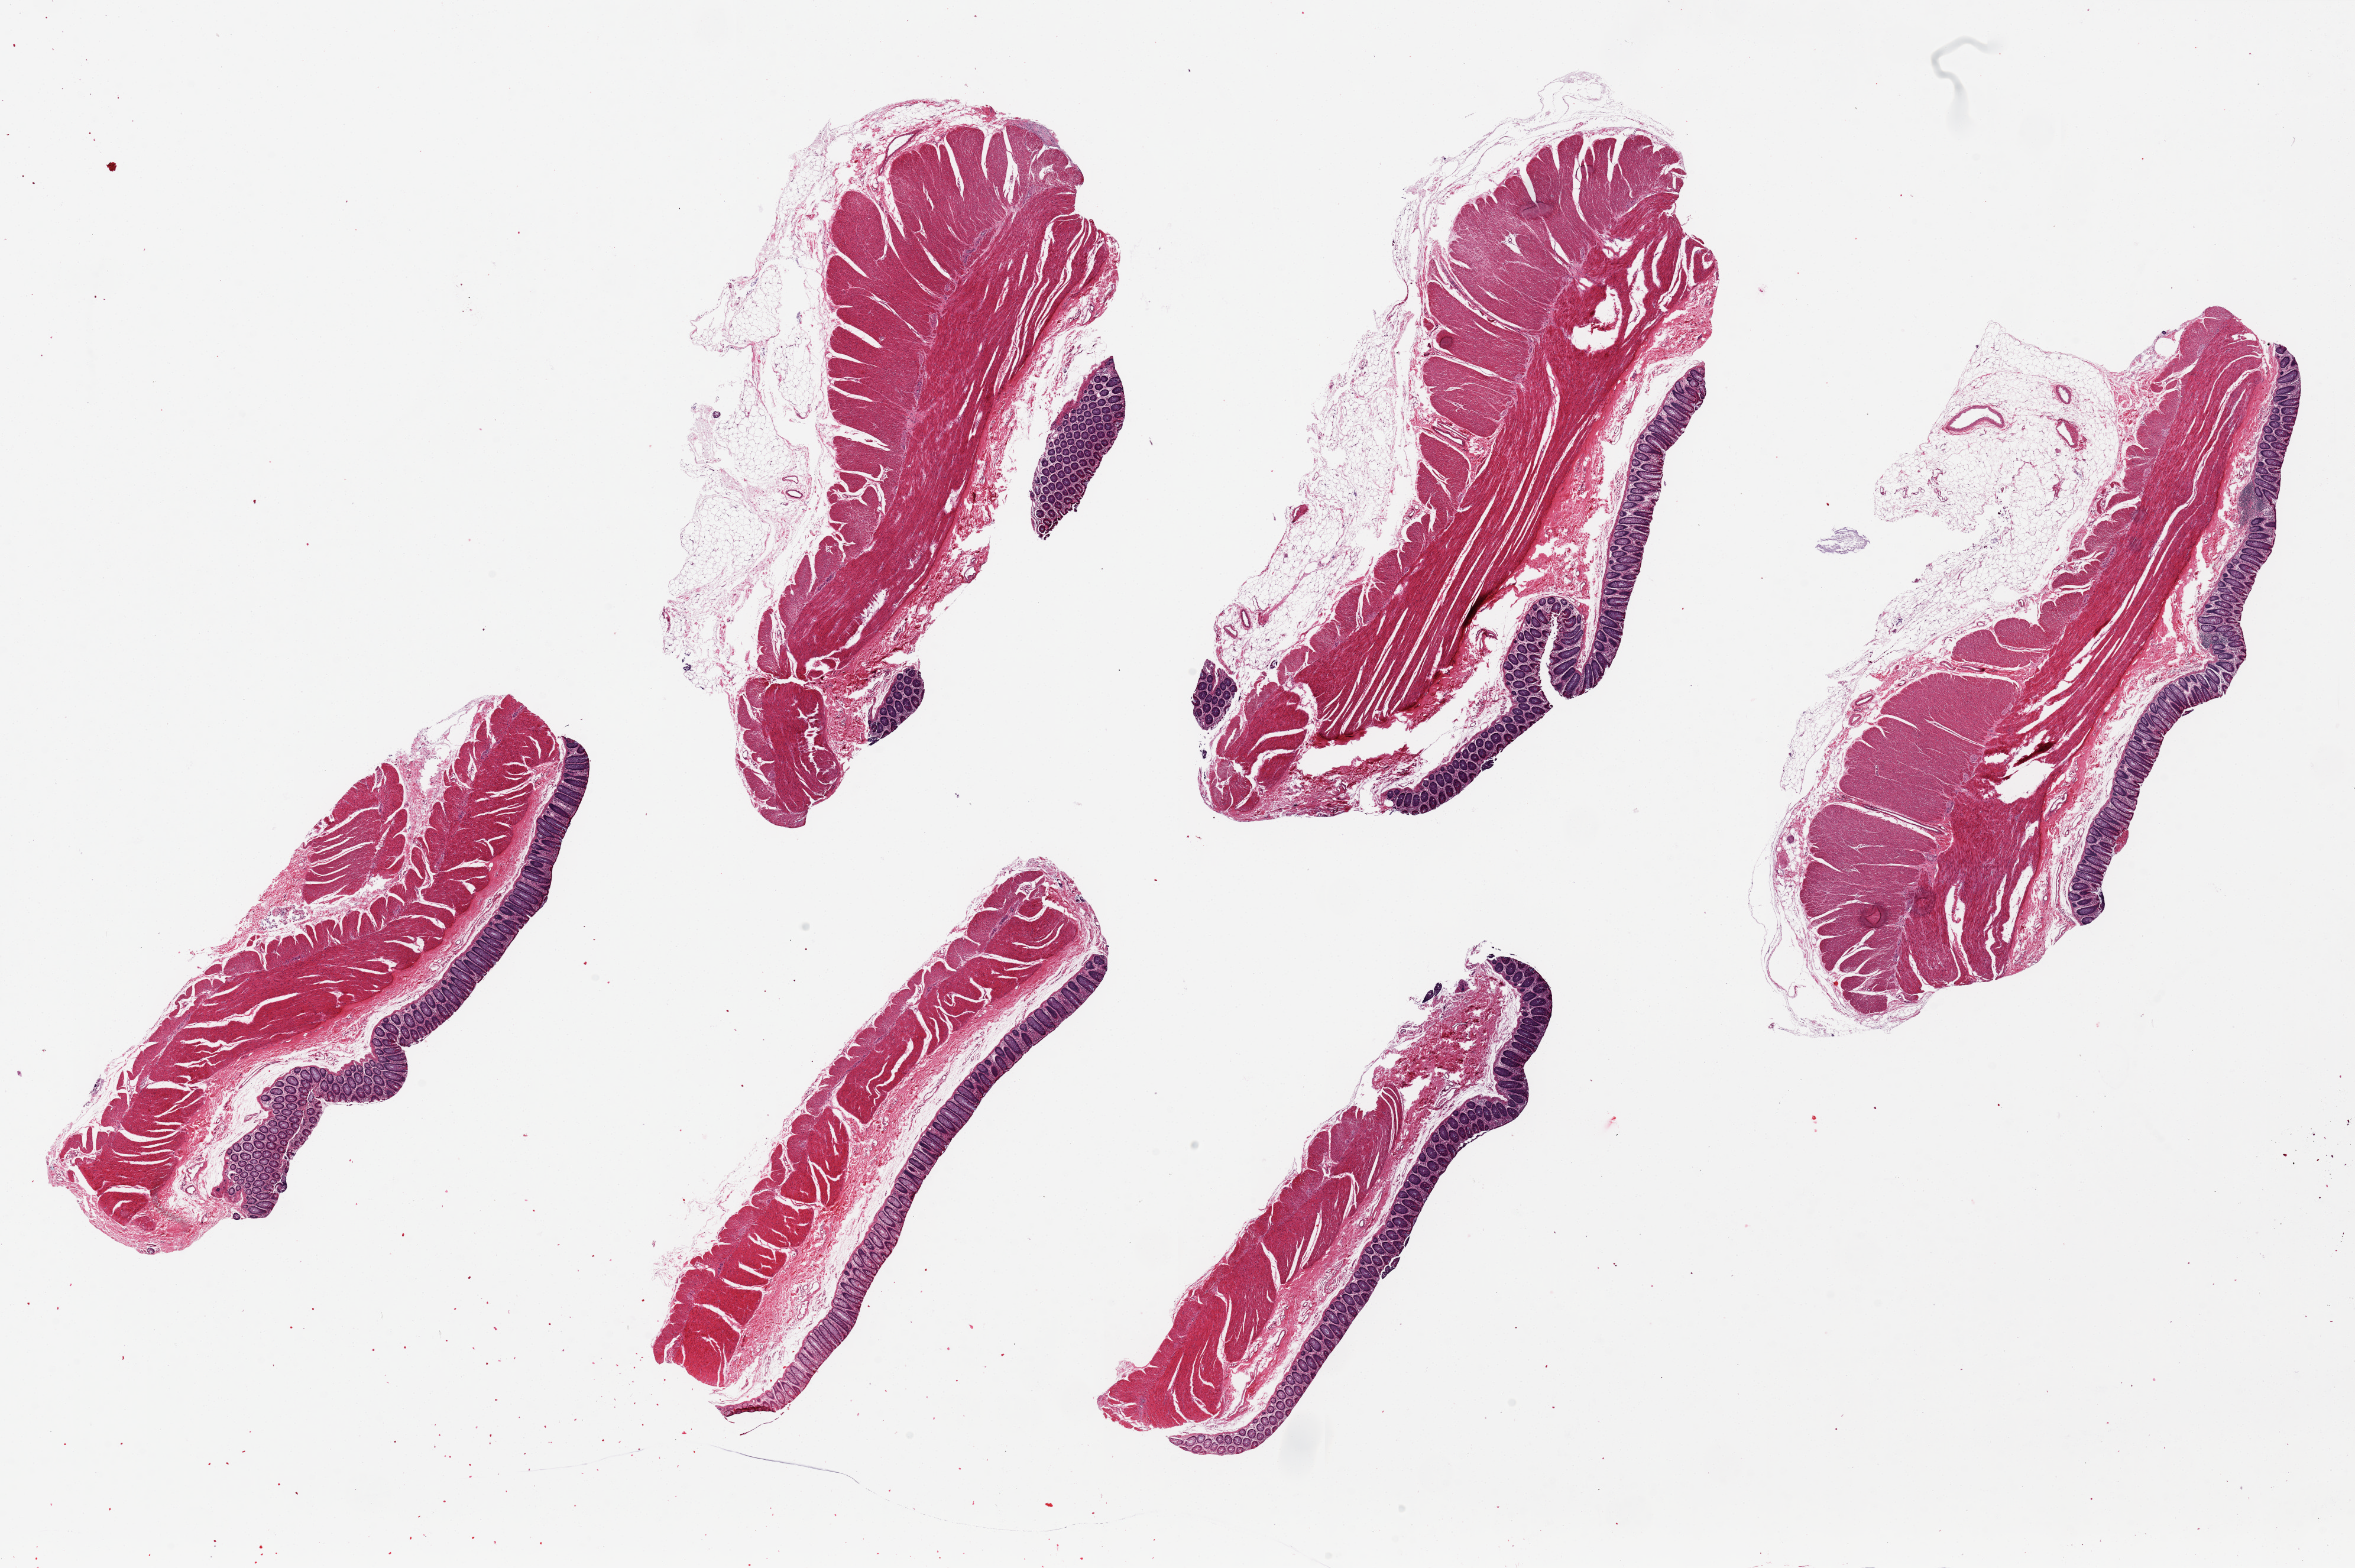
Whole-slide image, hematoxylin and eosin (H&E) stain, whole scanned area (about 31.5 x 21.0 mm, acquisition: 20x scan) shown as a low-resolution overview. PAXgene-fixed, paraffin-embedded tissue. Target tissue: transverse colon. Donor tissue sample. Donor sex: male.
Pathologist's review note for this sample: 6 pieces up to 10.5x4.6 mm; focal tissue tears.